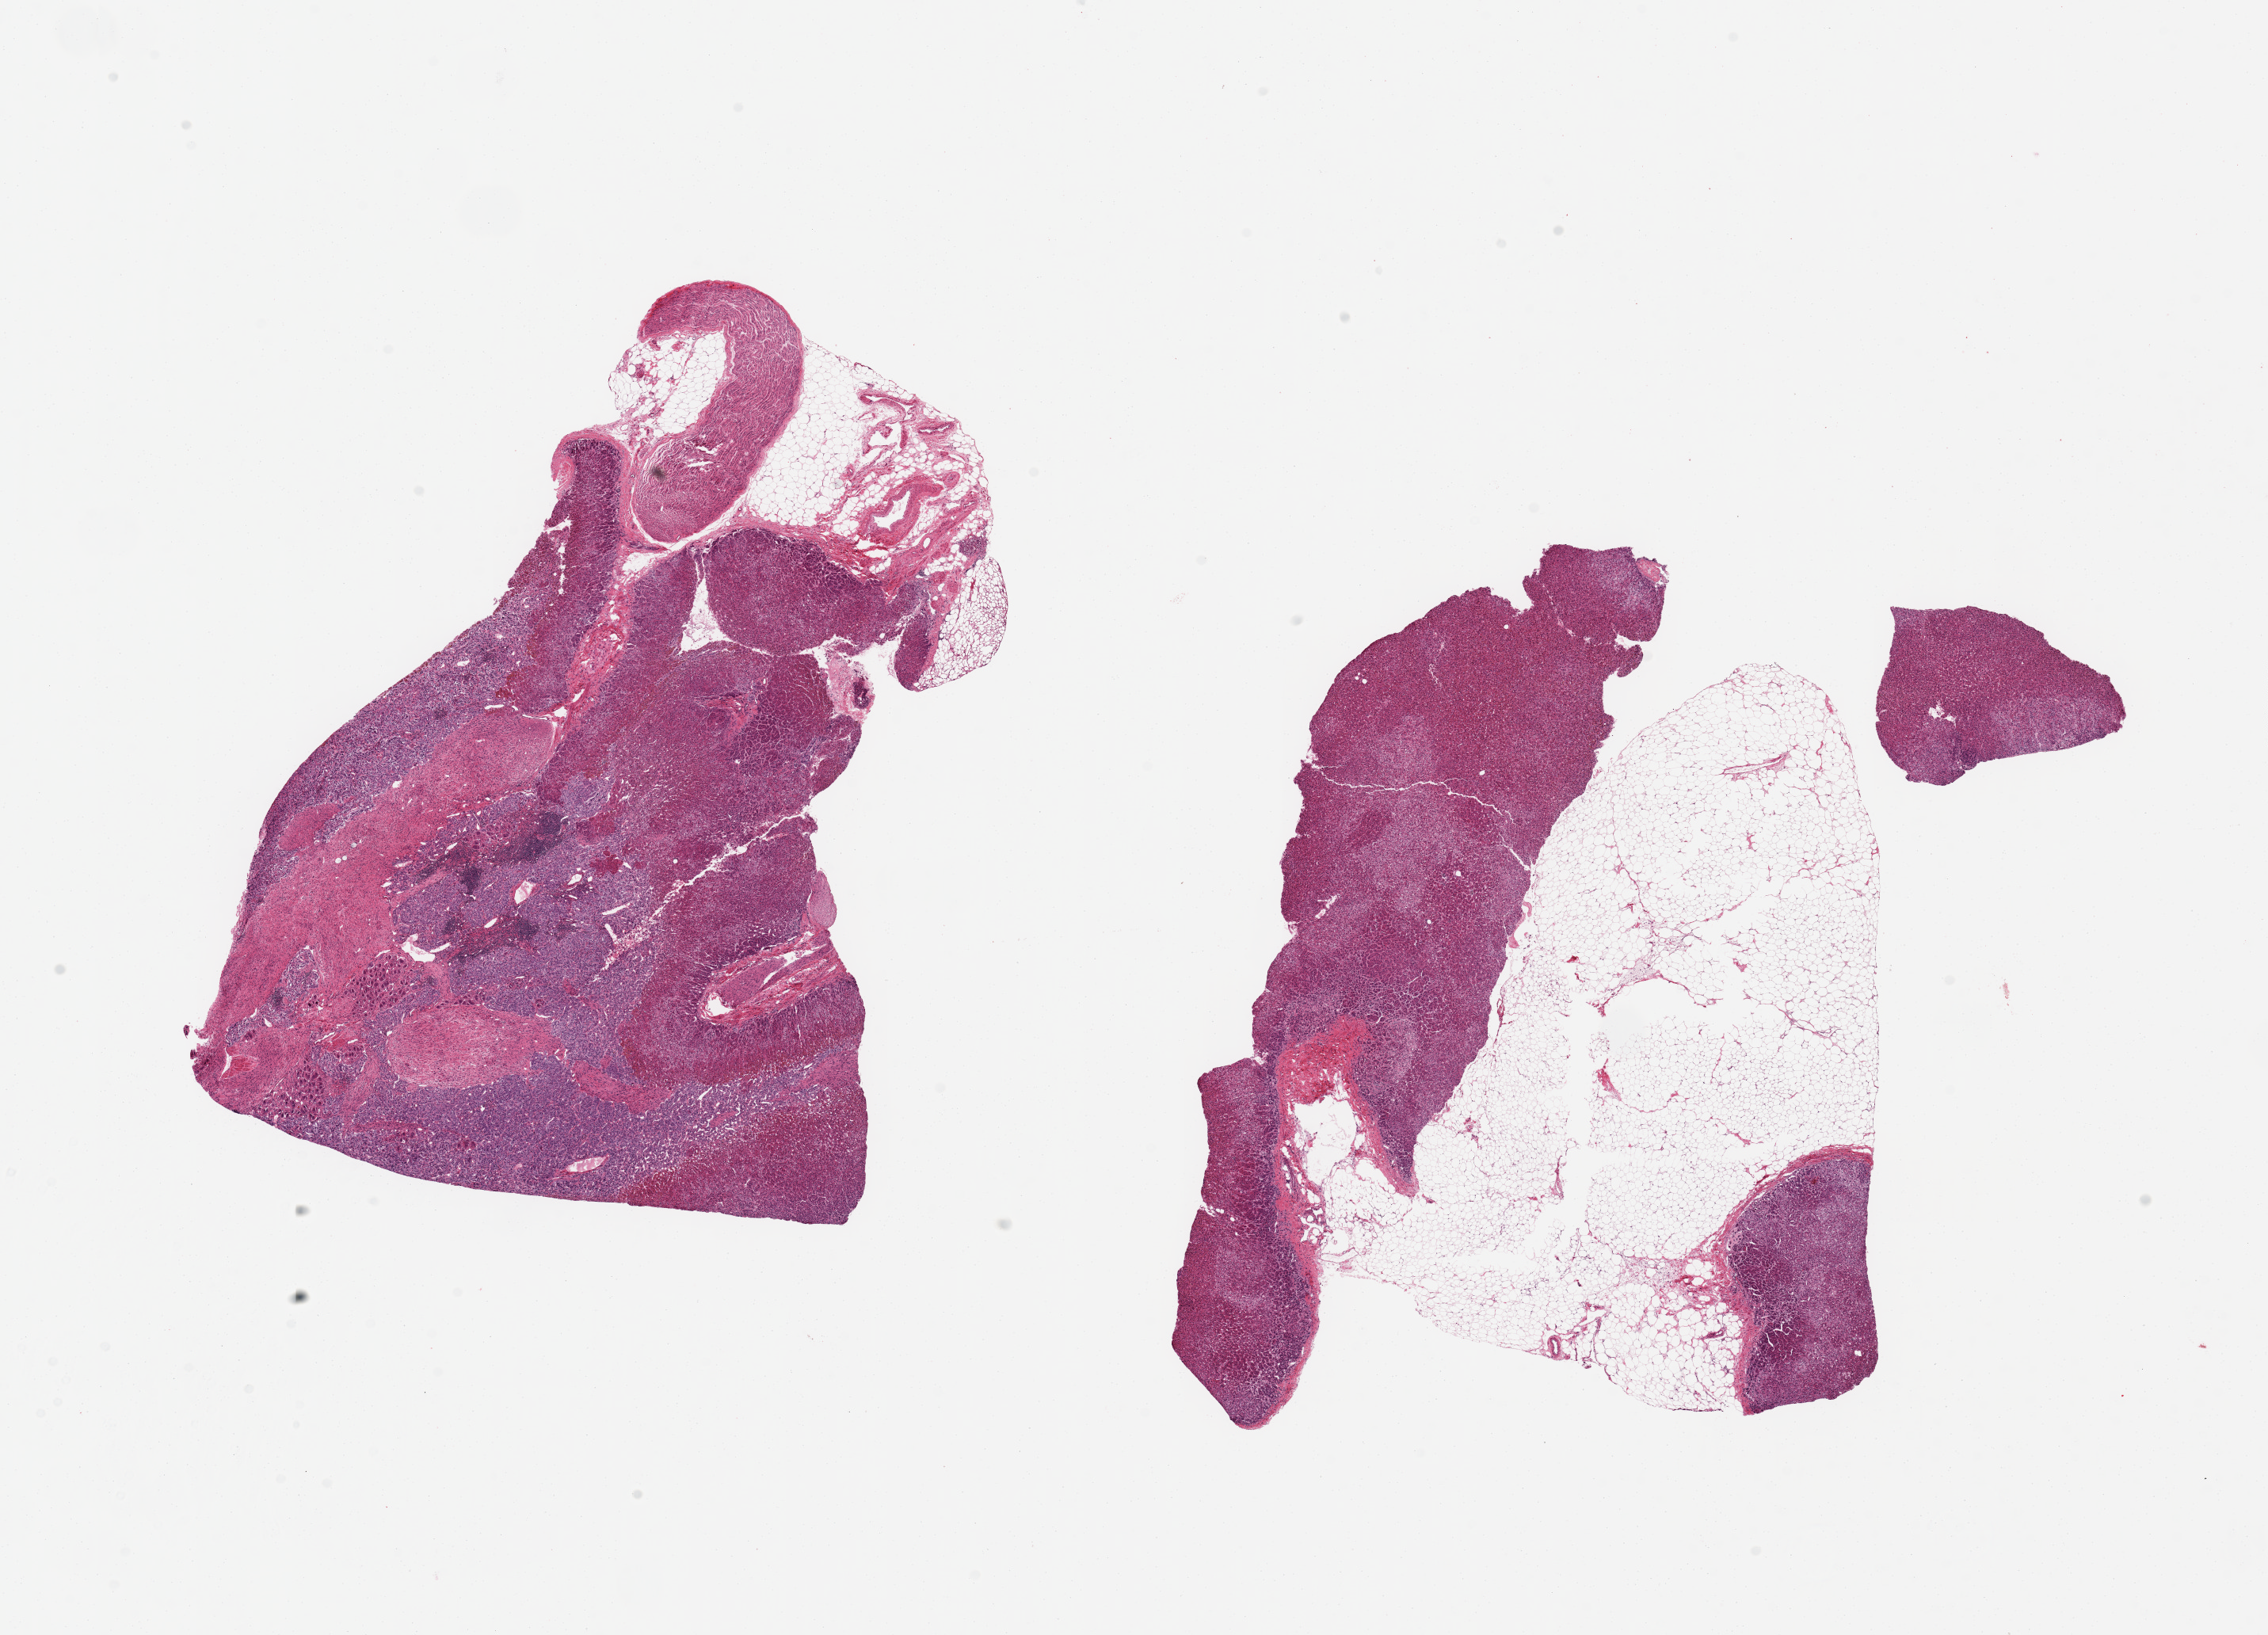
Digitized H&E-stained section, brightfield, whole scanned area (about 22.6 x 16.3 mm, slide scanned at 20x) shown as a low-resolution overview. PAXgene-fixed, paraffin-embedded tissue. Target tissue: adrenal gland. Tissue donor sample. Donor: male.
Pathologist's review note for this sample: 2 pieces, 9x7 & 9x7 mm; 1 with ~20% nerves and ganglion cells; other with 50% adipose tissue centrally.